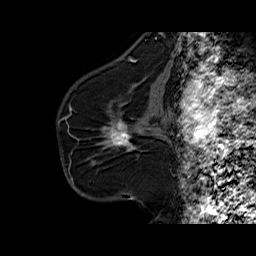
Breast MRI (dynamic contrast-enhanced), one sagittal slice; slice 38 of 60 in the series (ordered by position); dynamic contrast-enhanced series, time point 2 of 6 at this slice position (early post-contrast); 1.5 T; TE 6.3 ms, TR 32.5 ms; 4 mm slice thickness; 256 × 256 image matrix, field of view 200 × 200 mm. Female patient. From the clinical record (not read from this slice): setting: breast cancer imaged before/during neoadjuvant chemotherapy; receptor status: HR-positive, HER2-negative.
Outlined on this slice (semi-automatically segmented with operator editing):
- analysis volume of interest (the breast-tissue region the enhancement analysis was run in; not a lesion): box from (x=94, y=103) to (x=161, y=164) px
- tumour enhancement mask (voxels above the 100 % enhancement threshold inside the analysis volume of interest): (x=110, y=120)–(x=130, y=145)